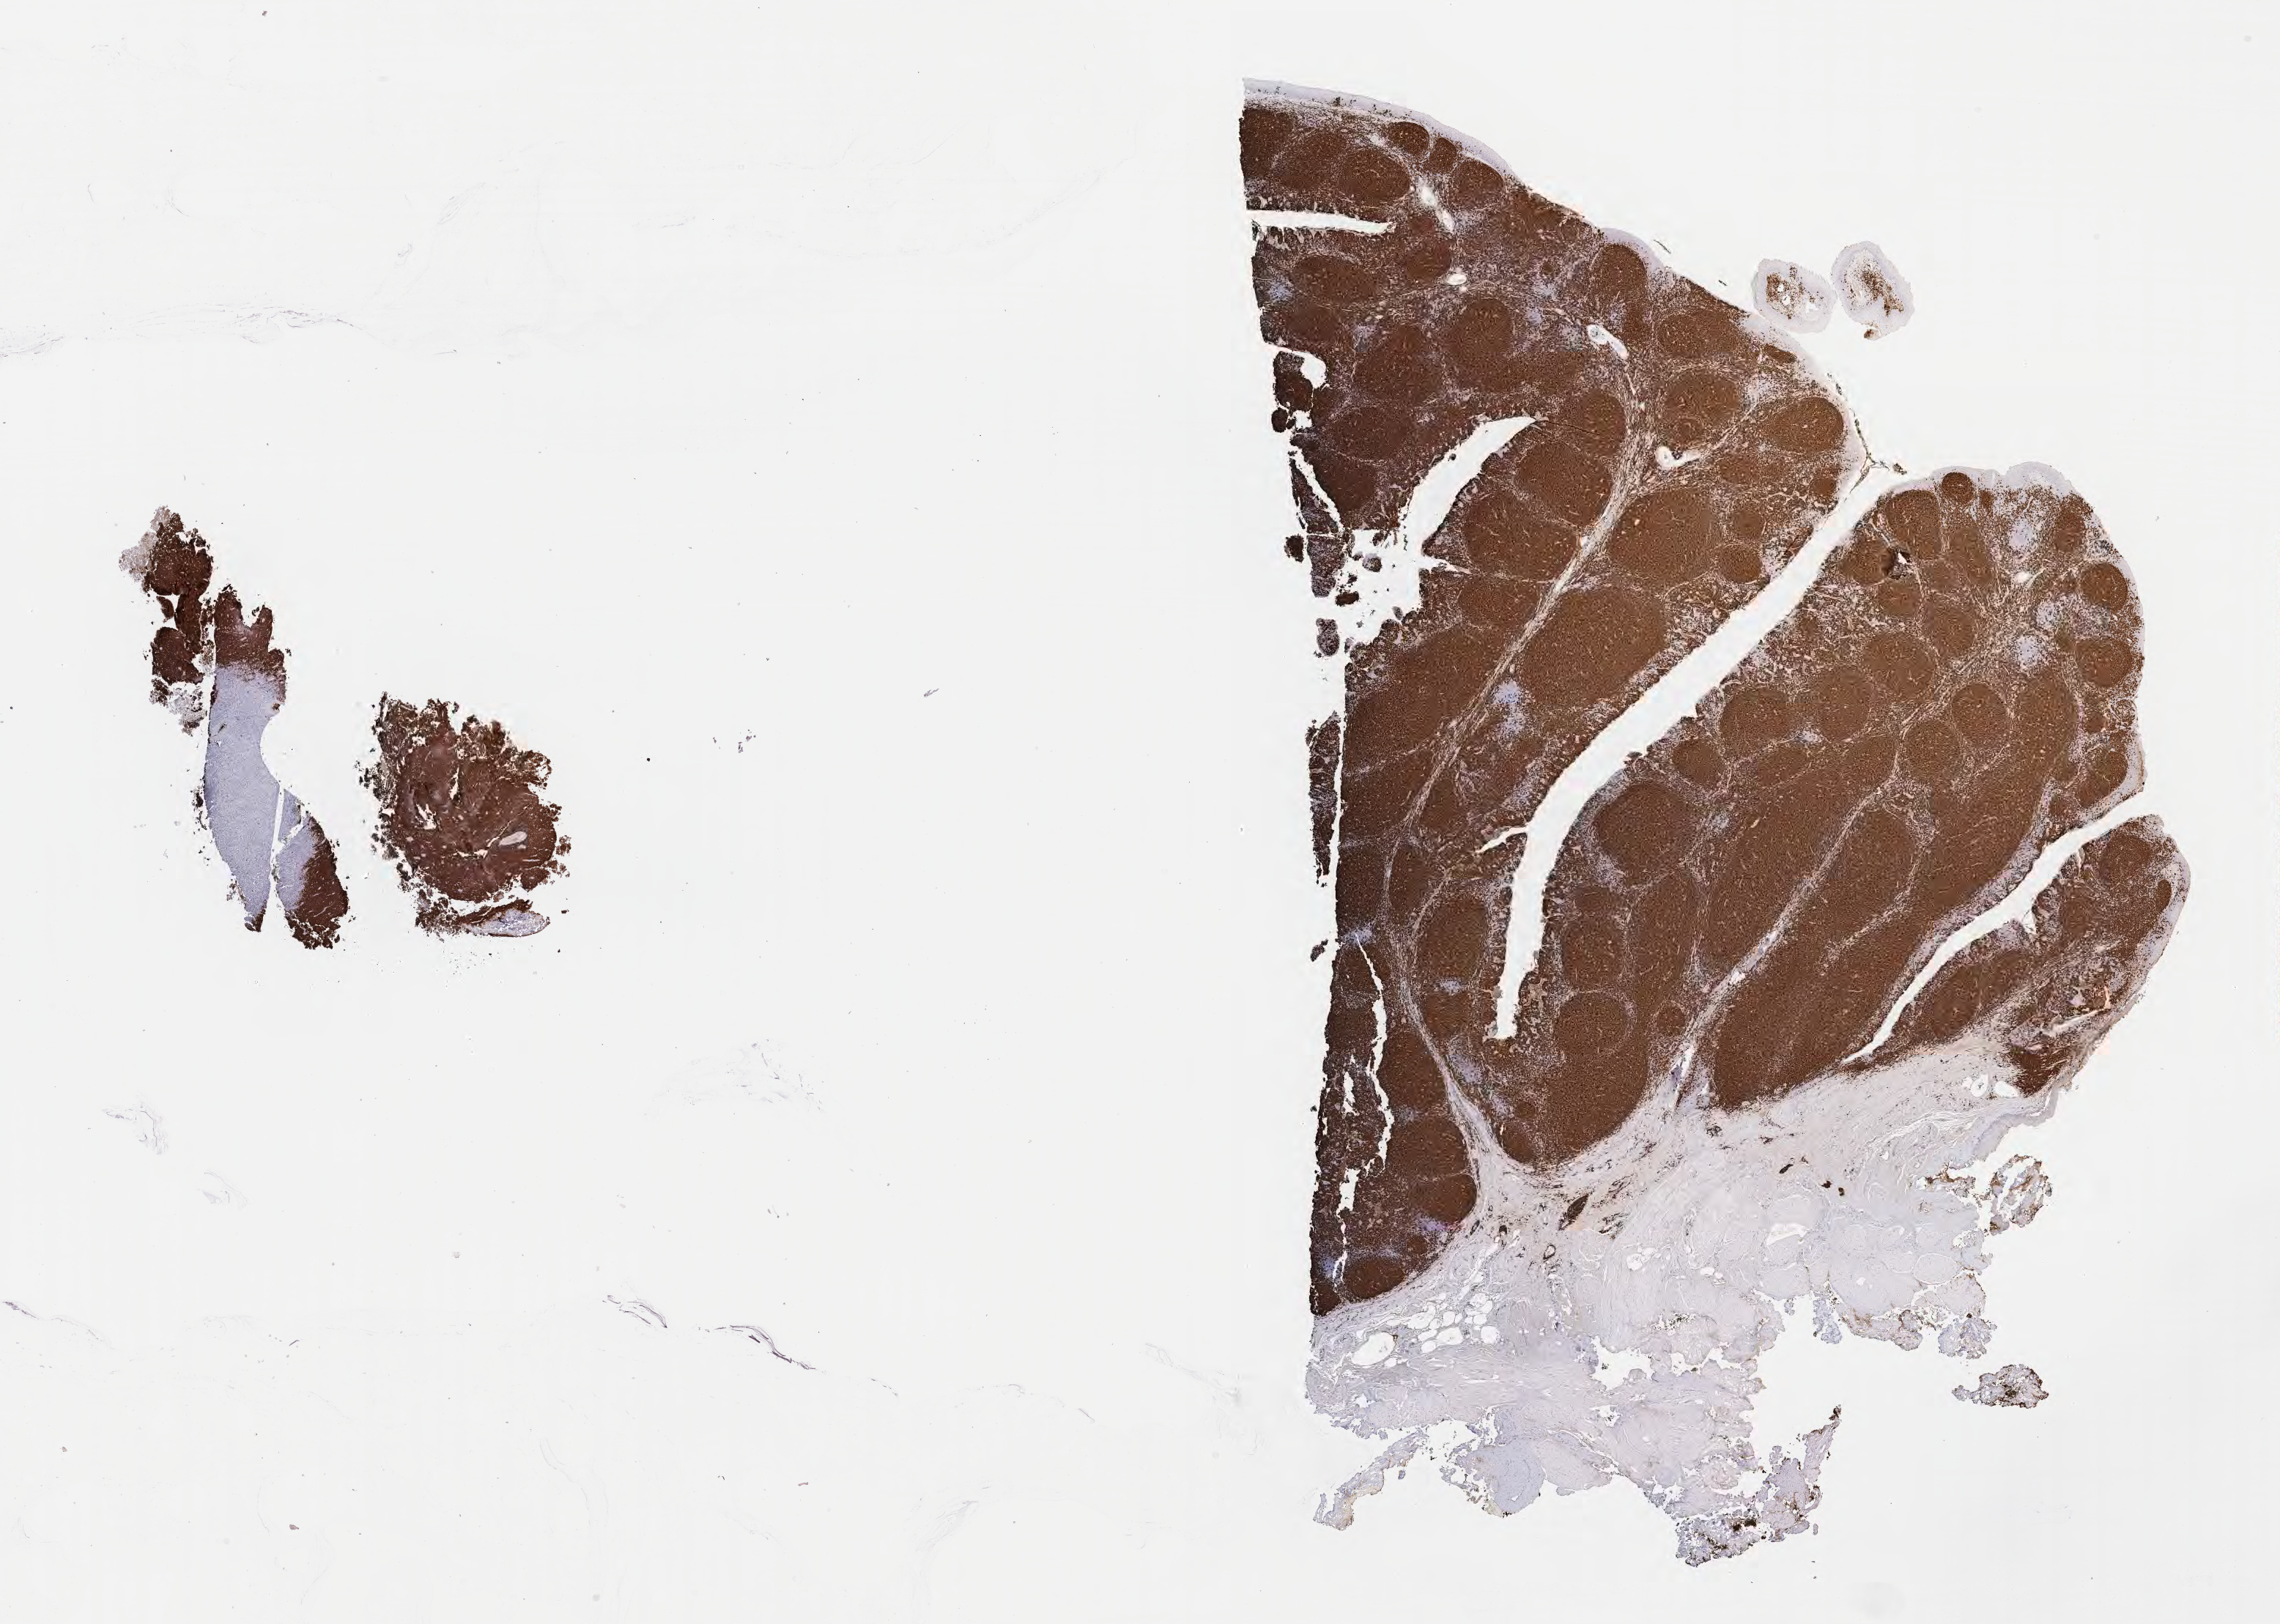
IHC for CD20, whole-slide image — whole scanned area (about 25.2 x 17.9 mm) shown as a low-resolution overview; specimen: tumor tissue; anatomic site: cranium. Male, age 4 years at initial diagnosis.
* diagnosis: Burkitt lymphoma, NOS